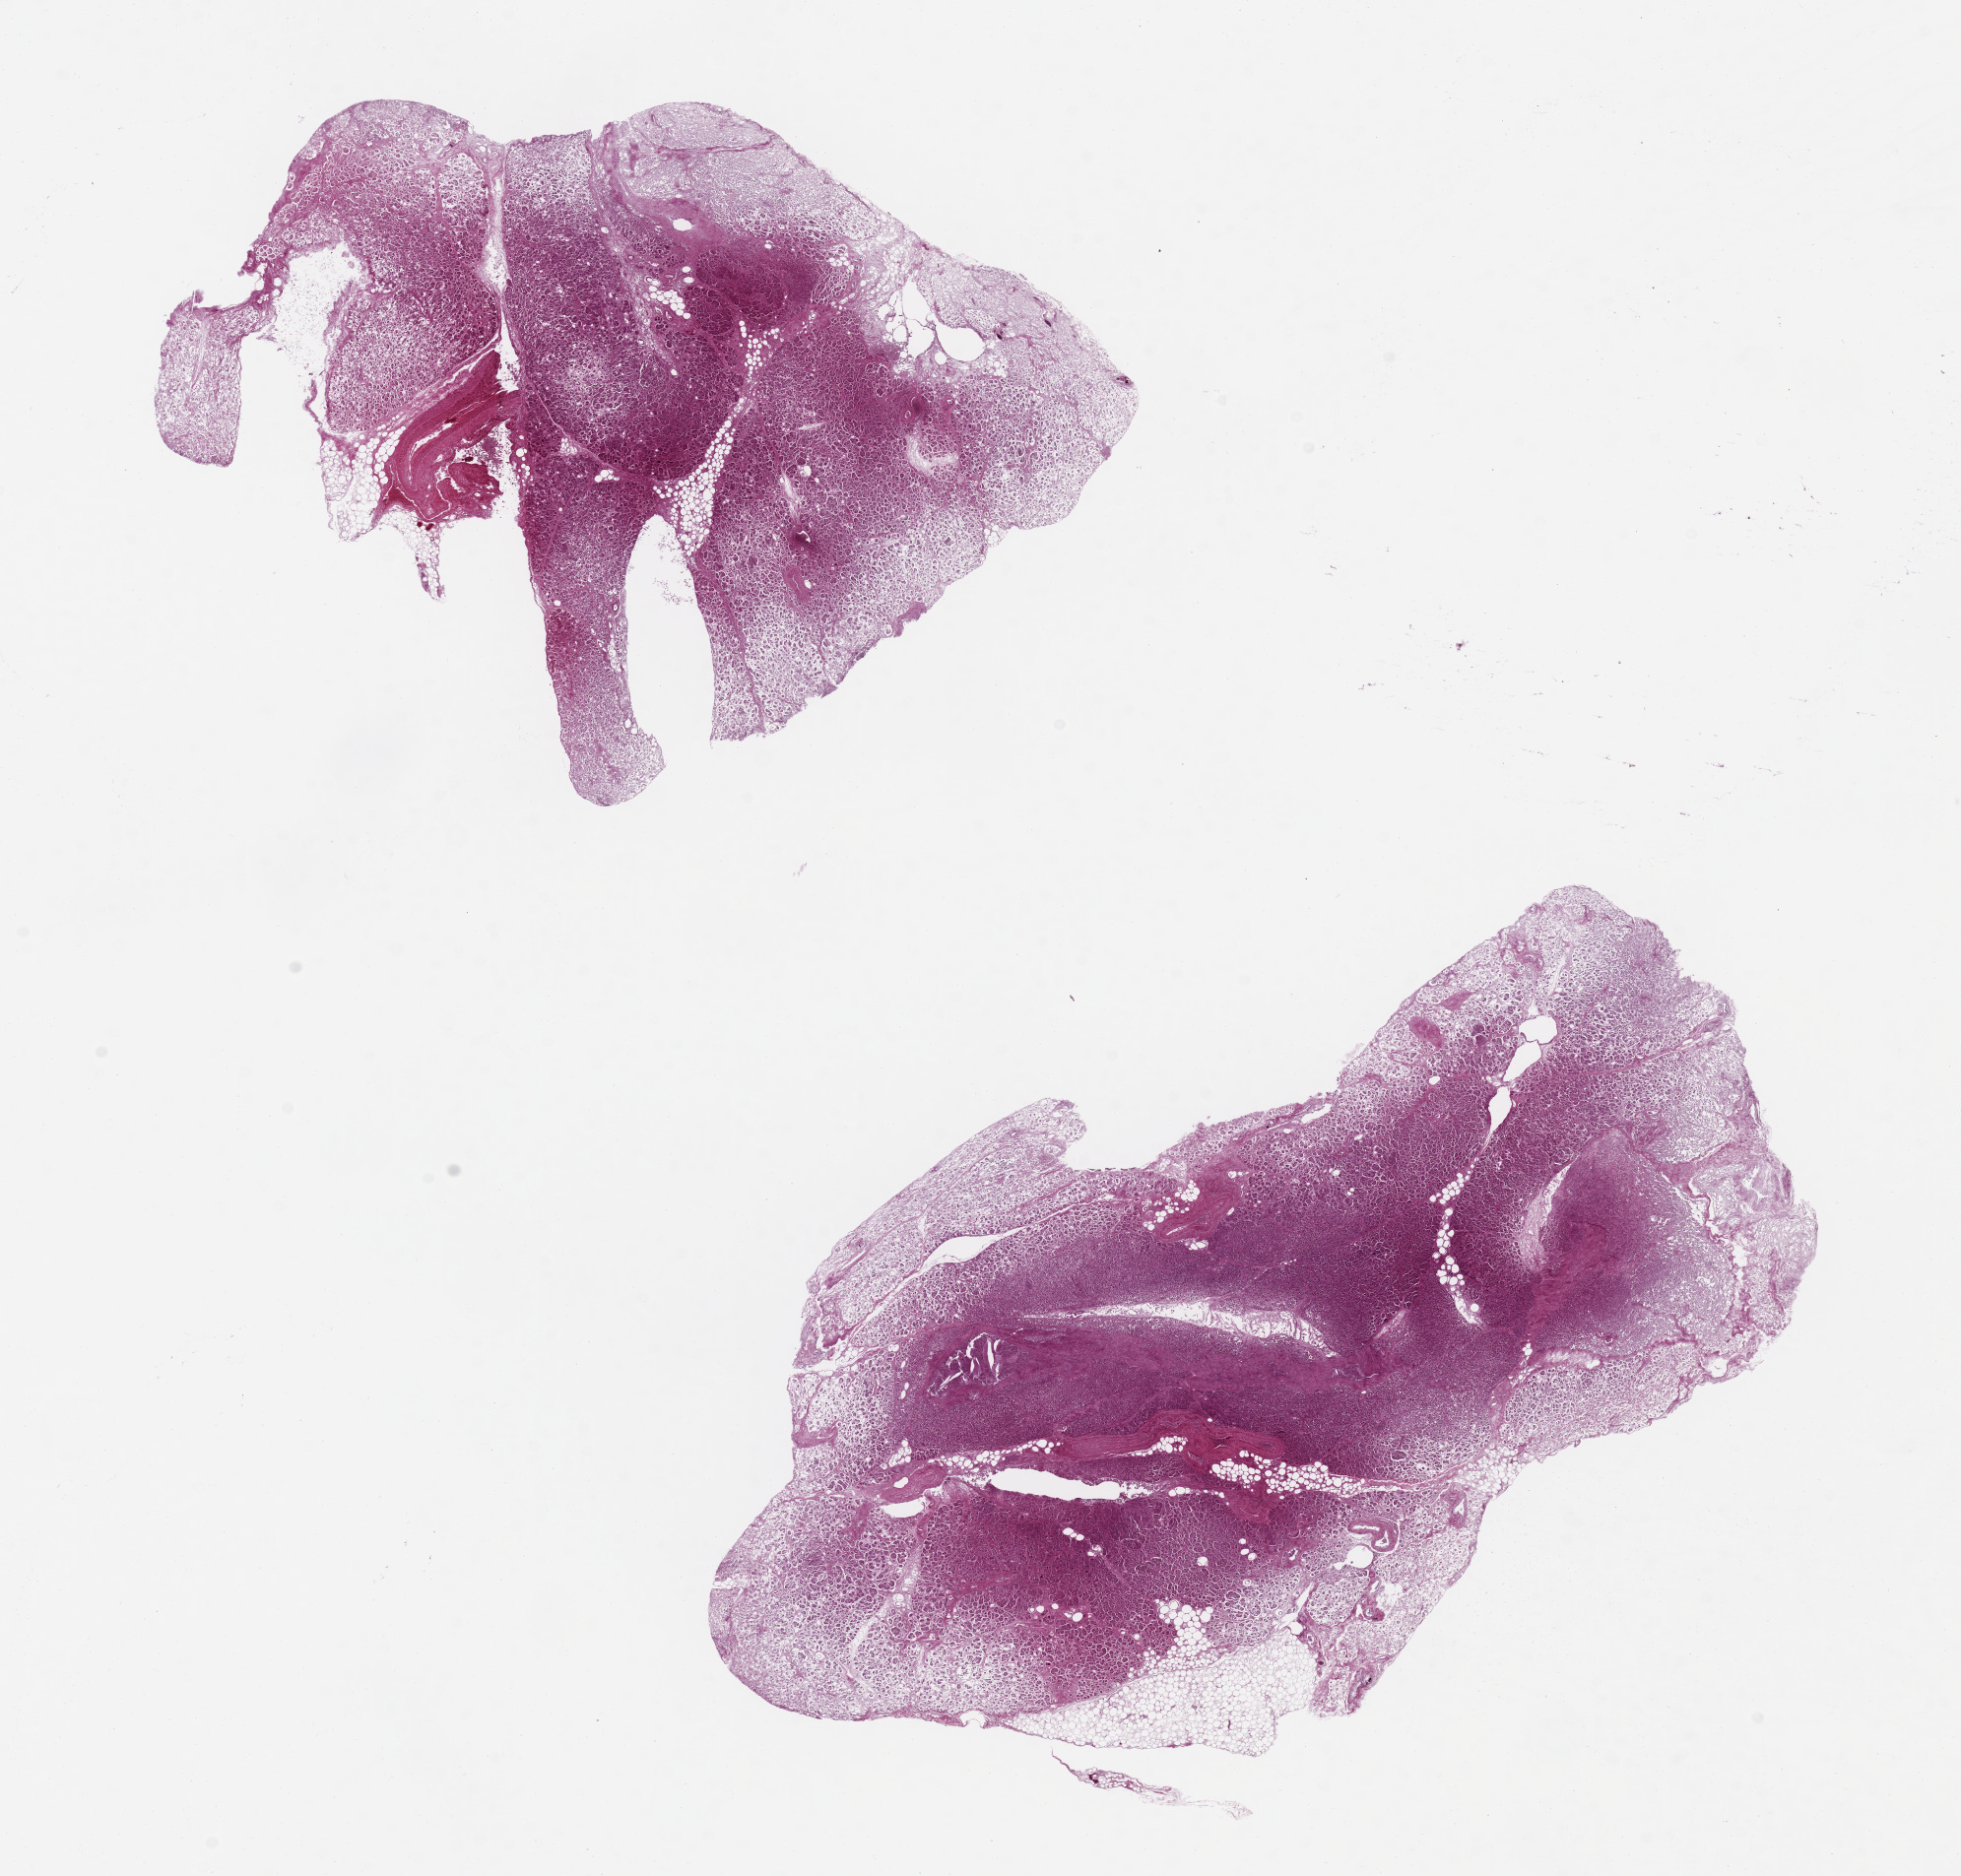
Hematoxylin and eosin (H&E) whole-slide image — a low-resolution overview of the entire scanned area, about 15.8 x 15.1 mm. PAXgene-fixed, paraffin-embedded tissue. Sampled site (target tissue): pancreas. Tissue donor sample. Male donor.
• review note (as recorded): 2 pieces, severe autolysis/post mortem saponification, ~8x4mm